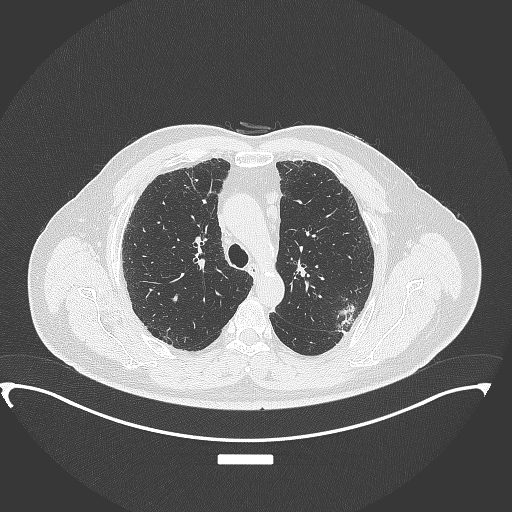
Chest CT, one axial slice; reconstruction kernel B70f; 120 kVp; lung window (W 1500 / L -600 HU); 1 mm slice thickness; 512 × 512 image matrix, field of view 459 × 459 mm. Patient: male, 64 years. Case-level facts recorded for this patient, not image findings: clinical TNM (as recorded): T1c N1 M1.
Annotated regions visible in this slice (bounding box drawn by a radiologist):
- lung tumour (recorded histology: adenocarcinoma): box from (x=336, y=301) to (x=360, y=339) px